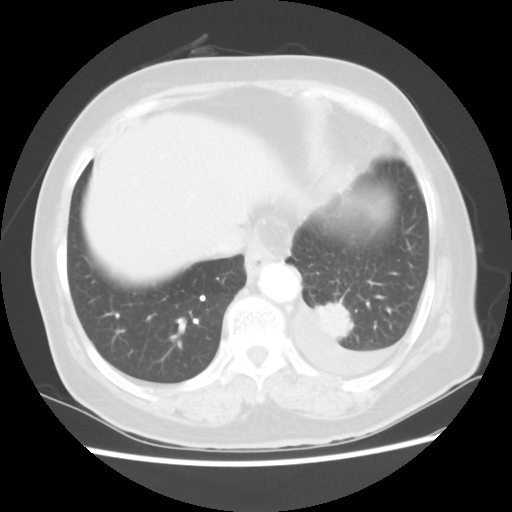
Chest CT, one axial slice. Slice 9 of 80 in the series (ordered by position). Reconstruction kernel STANDARD. Lung window (W 1500 / L -600 HU). 5 mm slice thickness. 512 × 512 image matrix, field of view 343 × 343 mm. Female patient, age 68 years. From the clinical record (not read from this slice): clinical TNM (as recorded): T1c N0 M1.
Outlined on this slice (rectangle marked by the reading radiologist):
- lung tumour (recorded histology: adenocarcinoma): box from (x=315, y=300) to (x=356, y=343) px